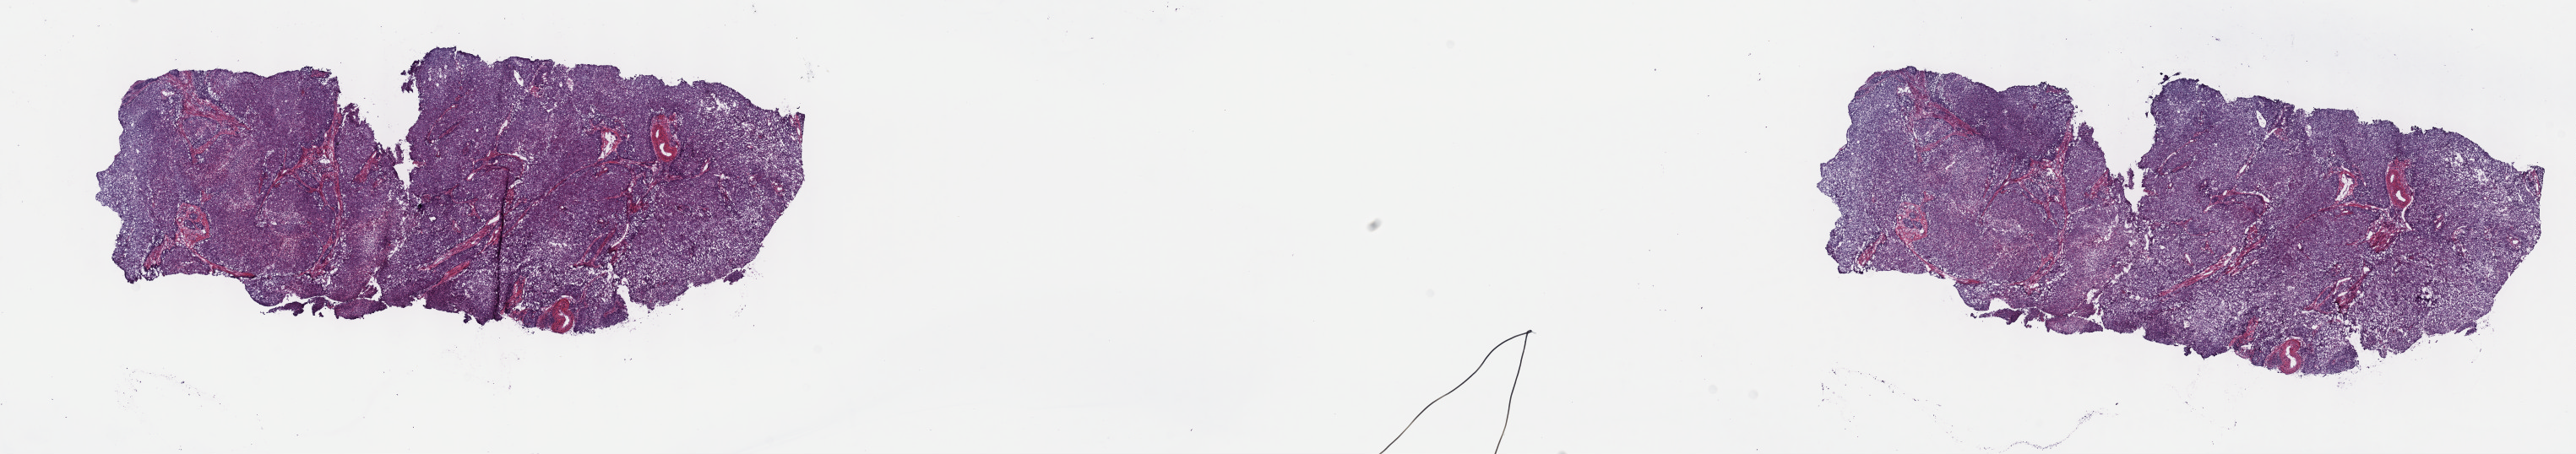
Digitized Hematoxylin and eosin (H&E) stained tissue section (whole slide) — whole scanned area (about 24.7 x 4.4 mm, acquisition: 40x scan) shown as a low-resolution overview, frozen section from the top of the tissue portion, cervix, primary tumour sample. Female, age 46 years at initial diagnosis. Histologic grade: G2 (moderately differentiated). Slide review estimates, as recorded: tumour cells 85%, tumour nuclei 85%, normal cells 5%, stromal cells 5%, necrosis 5%. Inflammatory infiltration, as recorded: lymphocyte infiltration 3%, monocyte infiltration 0%, neutrophil infiltration 2%.
* pathologic diagnosis: Squamous cell carcinoma, large cell, nonkeratinizing, NOS (cervix uteri)
* lymph nodes positive (case pathology): 0 of 15 examined
* FIGO stage: IB1